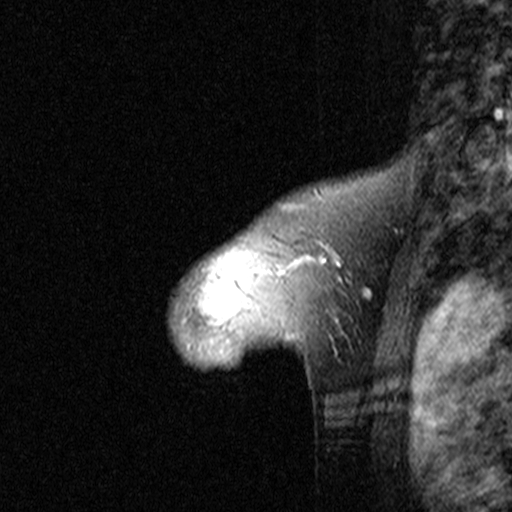
Breast MRI (dynamic contrast-enhanced), one sagittal slice. Position 34 of 44 along the scan axis. Dynamic contrast-enhanced study with each time point stored as its own series, time point 2 of 3 at this slice position (early post-contrast, ordered by acquisition time). 1.5 T. TE 4.5 ms, TR 11 ms. 3 mm slice thickness. 512 × 512 image matrix, field of view 200 × 200 mm. Female patient, age 46 years. Case-level facts recorded for this patient, not image findings: setting: breast cancer imaged before/during neoadjuvant chemotherapy; receptor status: HER2-positive.
Structures marked on this image (semi-automatically segmented with operator editing):
- analysis volume of interest (the breast-tissue region the enhancement analysis was run in; not a lesion): bounding box <154,172,359,393> (left, top, right, bottom; pixels)
- tumour enhancement mask (voxels above the 90 % enhancement threshold inside the analysis volume of interest): <284,241,342,340>